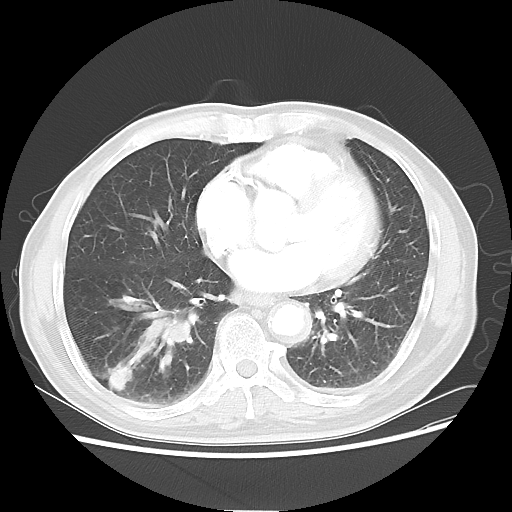
Chest CT, one axial slice; position 24 of 58 along the scan axis; reconstruction kernel LUNG; 120 kVp; lung window (W 1500 / L -600 HU); 5 mm slice thickness; 512 × 512 image matrix, field of view 360 × 360 mm. Male patient, age 74 years. Case-level facts recorded for this patient, not image findings: clinical TNM (as recorded): T1c N1 M1.
Structures marked on this image (rectangle marked by the reading radiologist):
- lung tumour (recorded histology: adenocarcinoma): bounding box <131,296,198,369> (left, top, right, bottom; pixels)